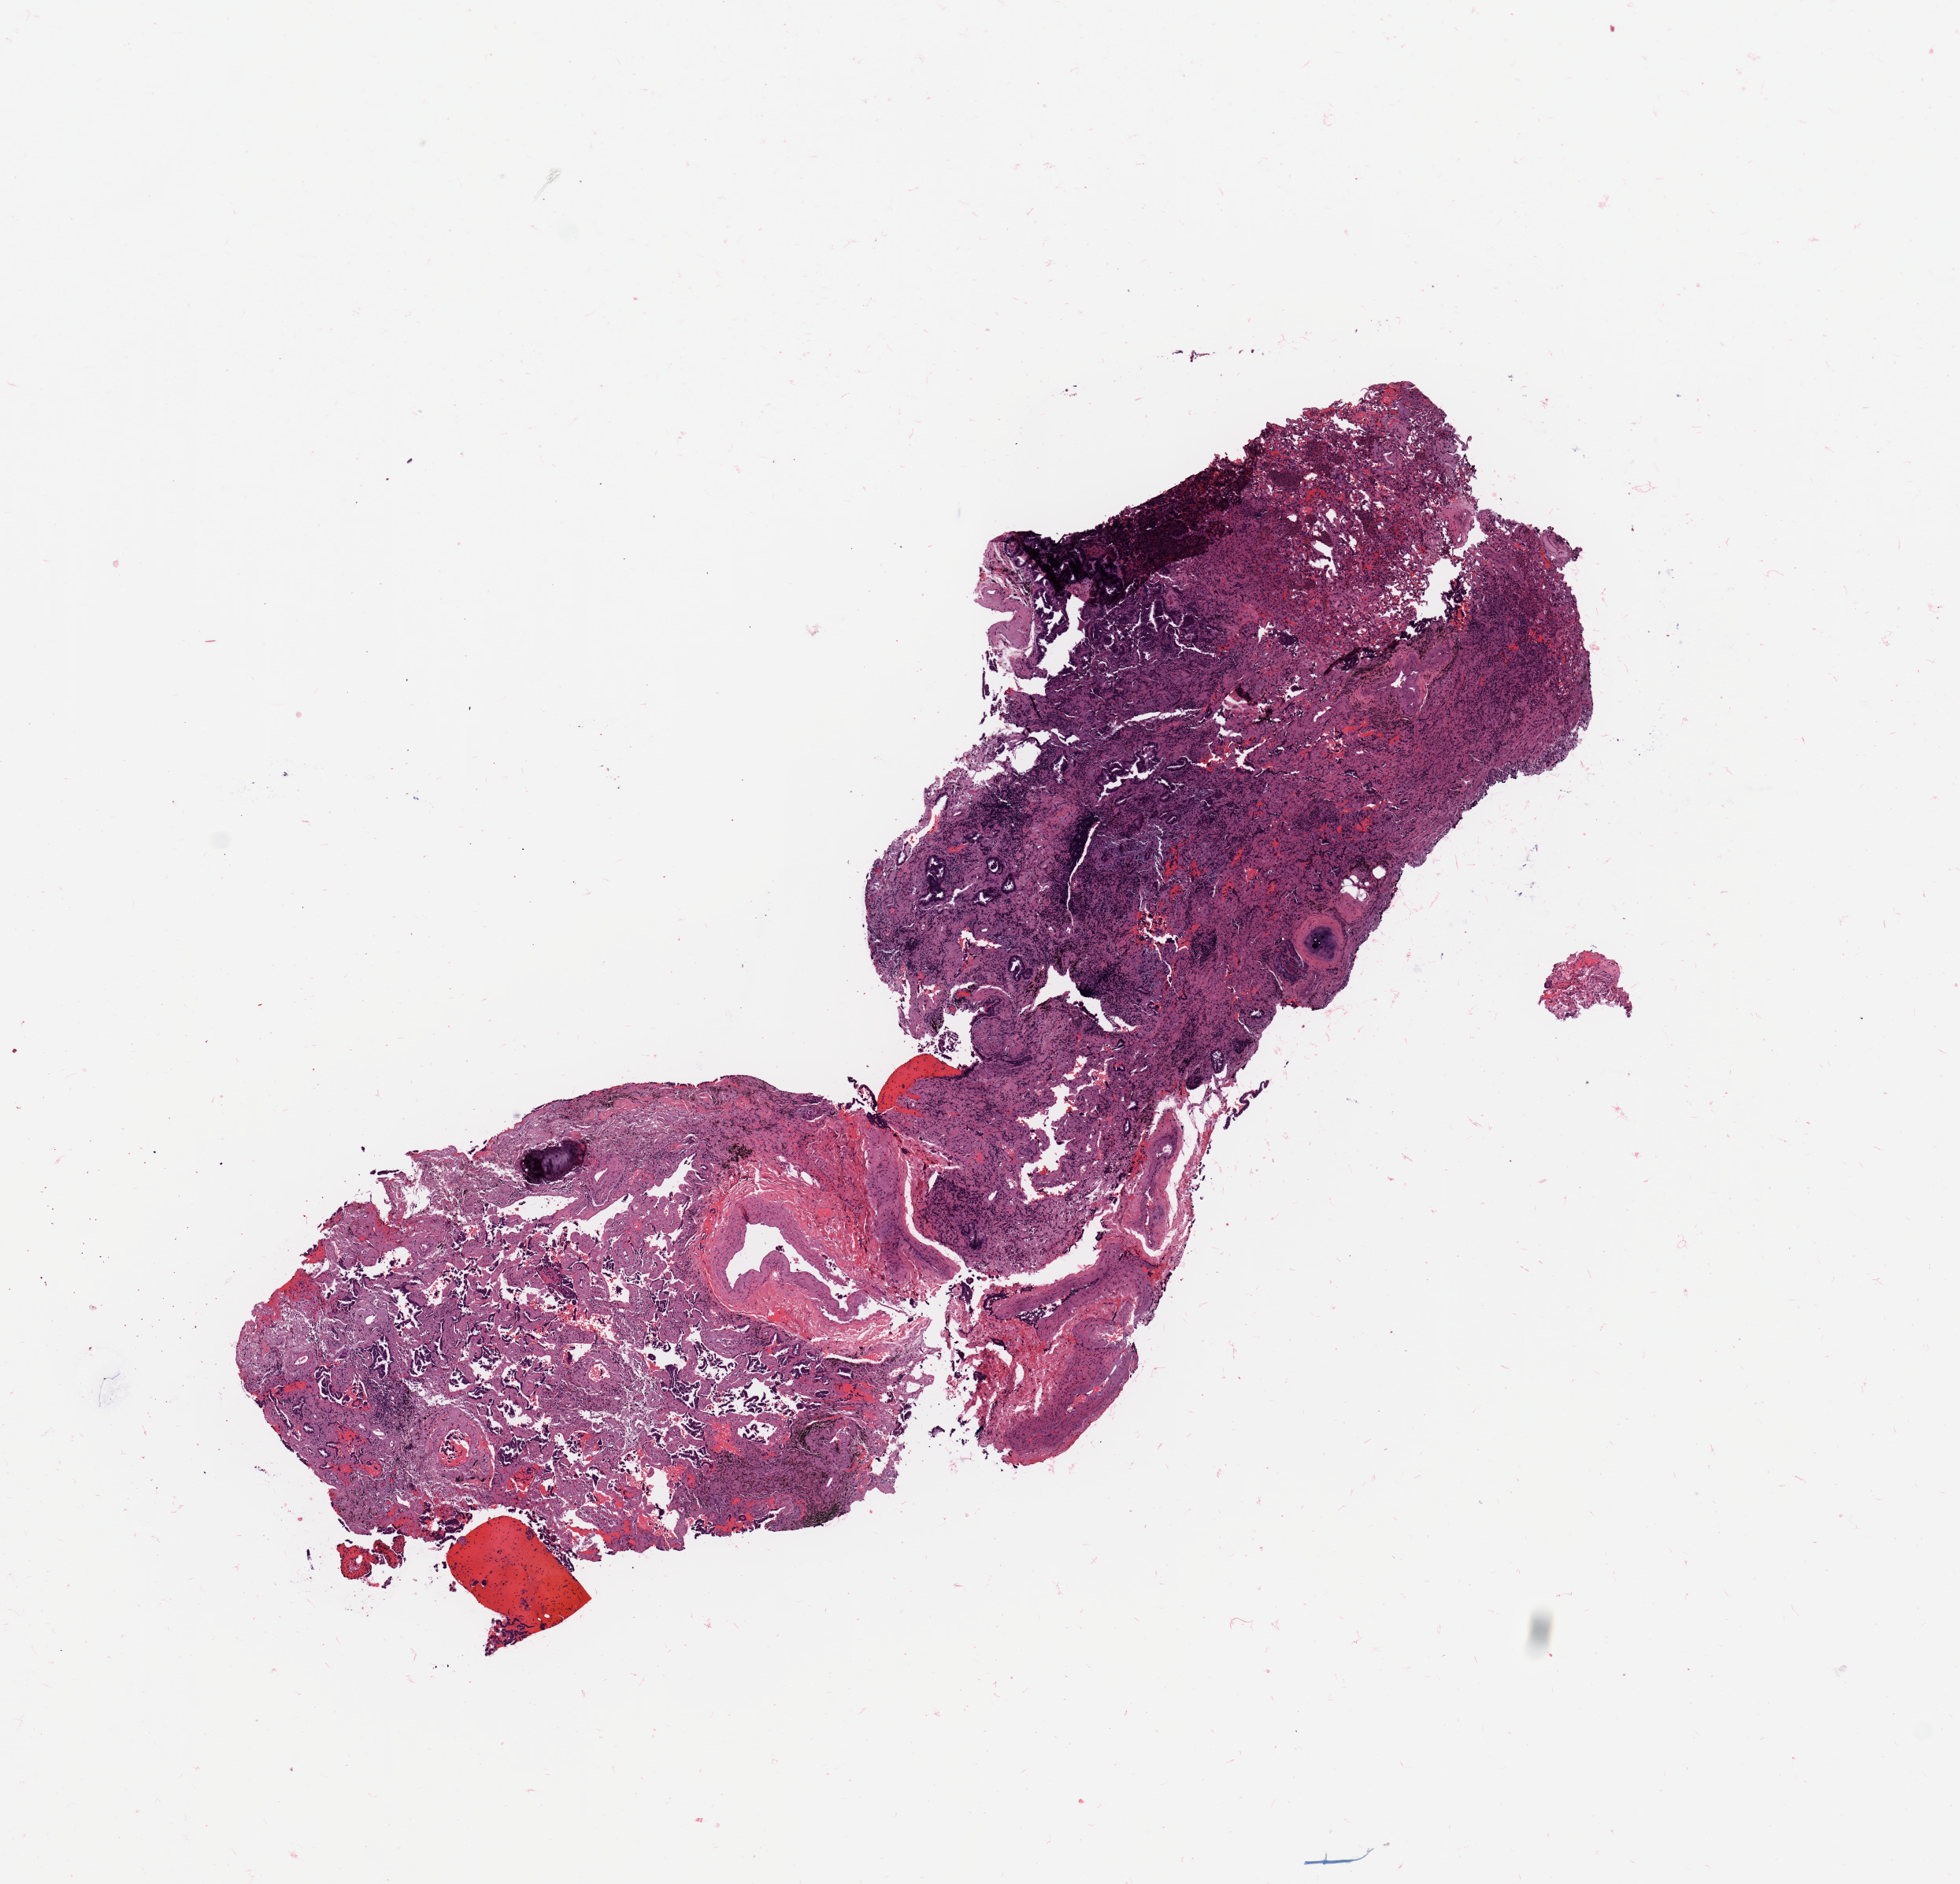
H&E whole-slide image — a low-resolution overview of the entire scanned area, about 9.8 x 9.5 mm (slide scanned at 20x); lung, tumour tissue. 71-year-old male patient.
Diagnosis: Adenocarcinoma, NOS.